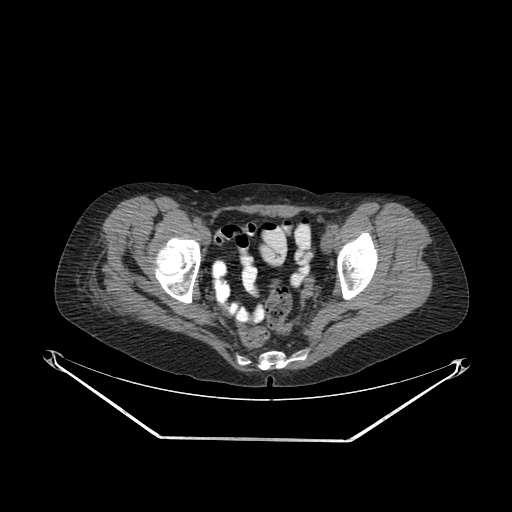
CT of an extremity soft-tissue mass (from a PET/CT study), one axial slice; position 56 of 267 along the scan axis; 140 kVp; soft-tissue window (W 400 / L 40 HU); 3.75 mm slice thickness; 512 × 512 image matrix, field of view 500 × 500 mm. Female patient. From the clinical record (not read from this slice): histological type: epithelioid sarcoma with vascular differentiation; site of the primary tumour: right buttock.
Annotated regions visible in this slice (expert contour drawn on MRI and transferred to this co-registered scan by the dataset authors):
- gross tumour volume (mass): bounding box [x1, y1, x2, y2] px = [84, 272, 131, 302]